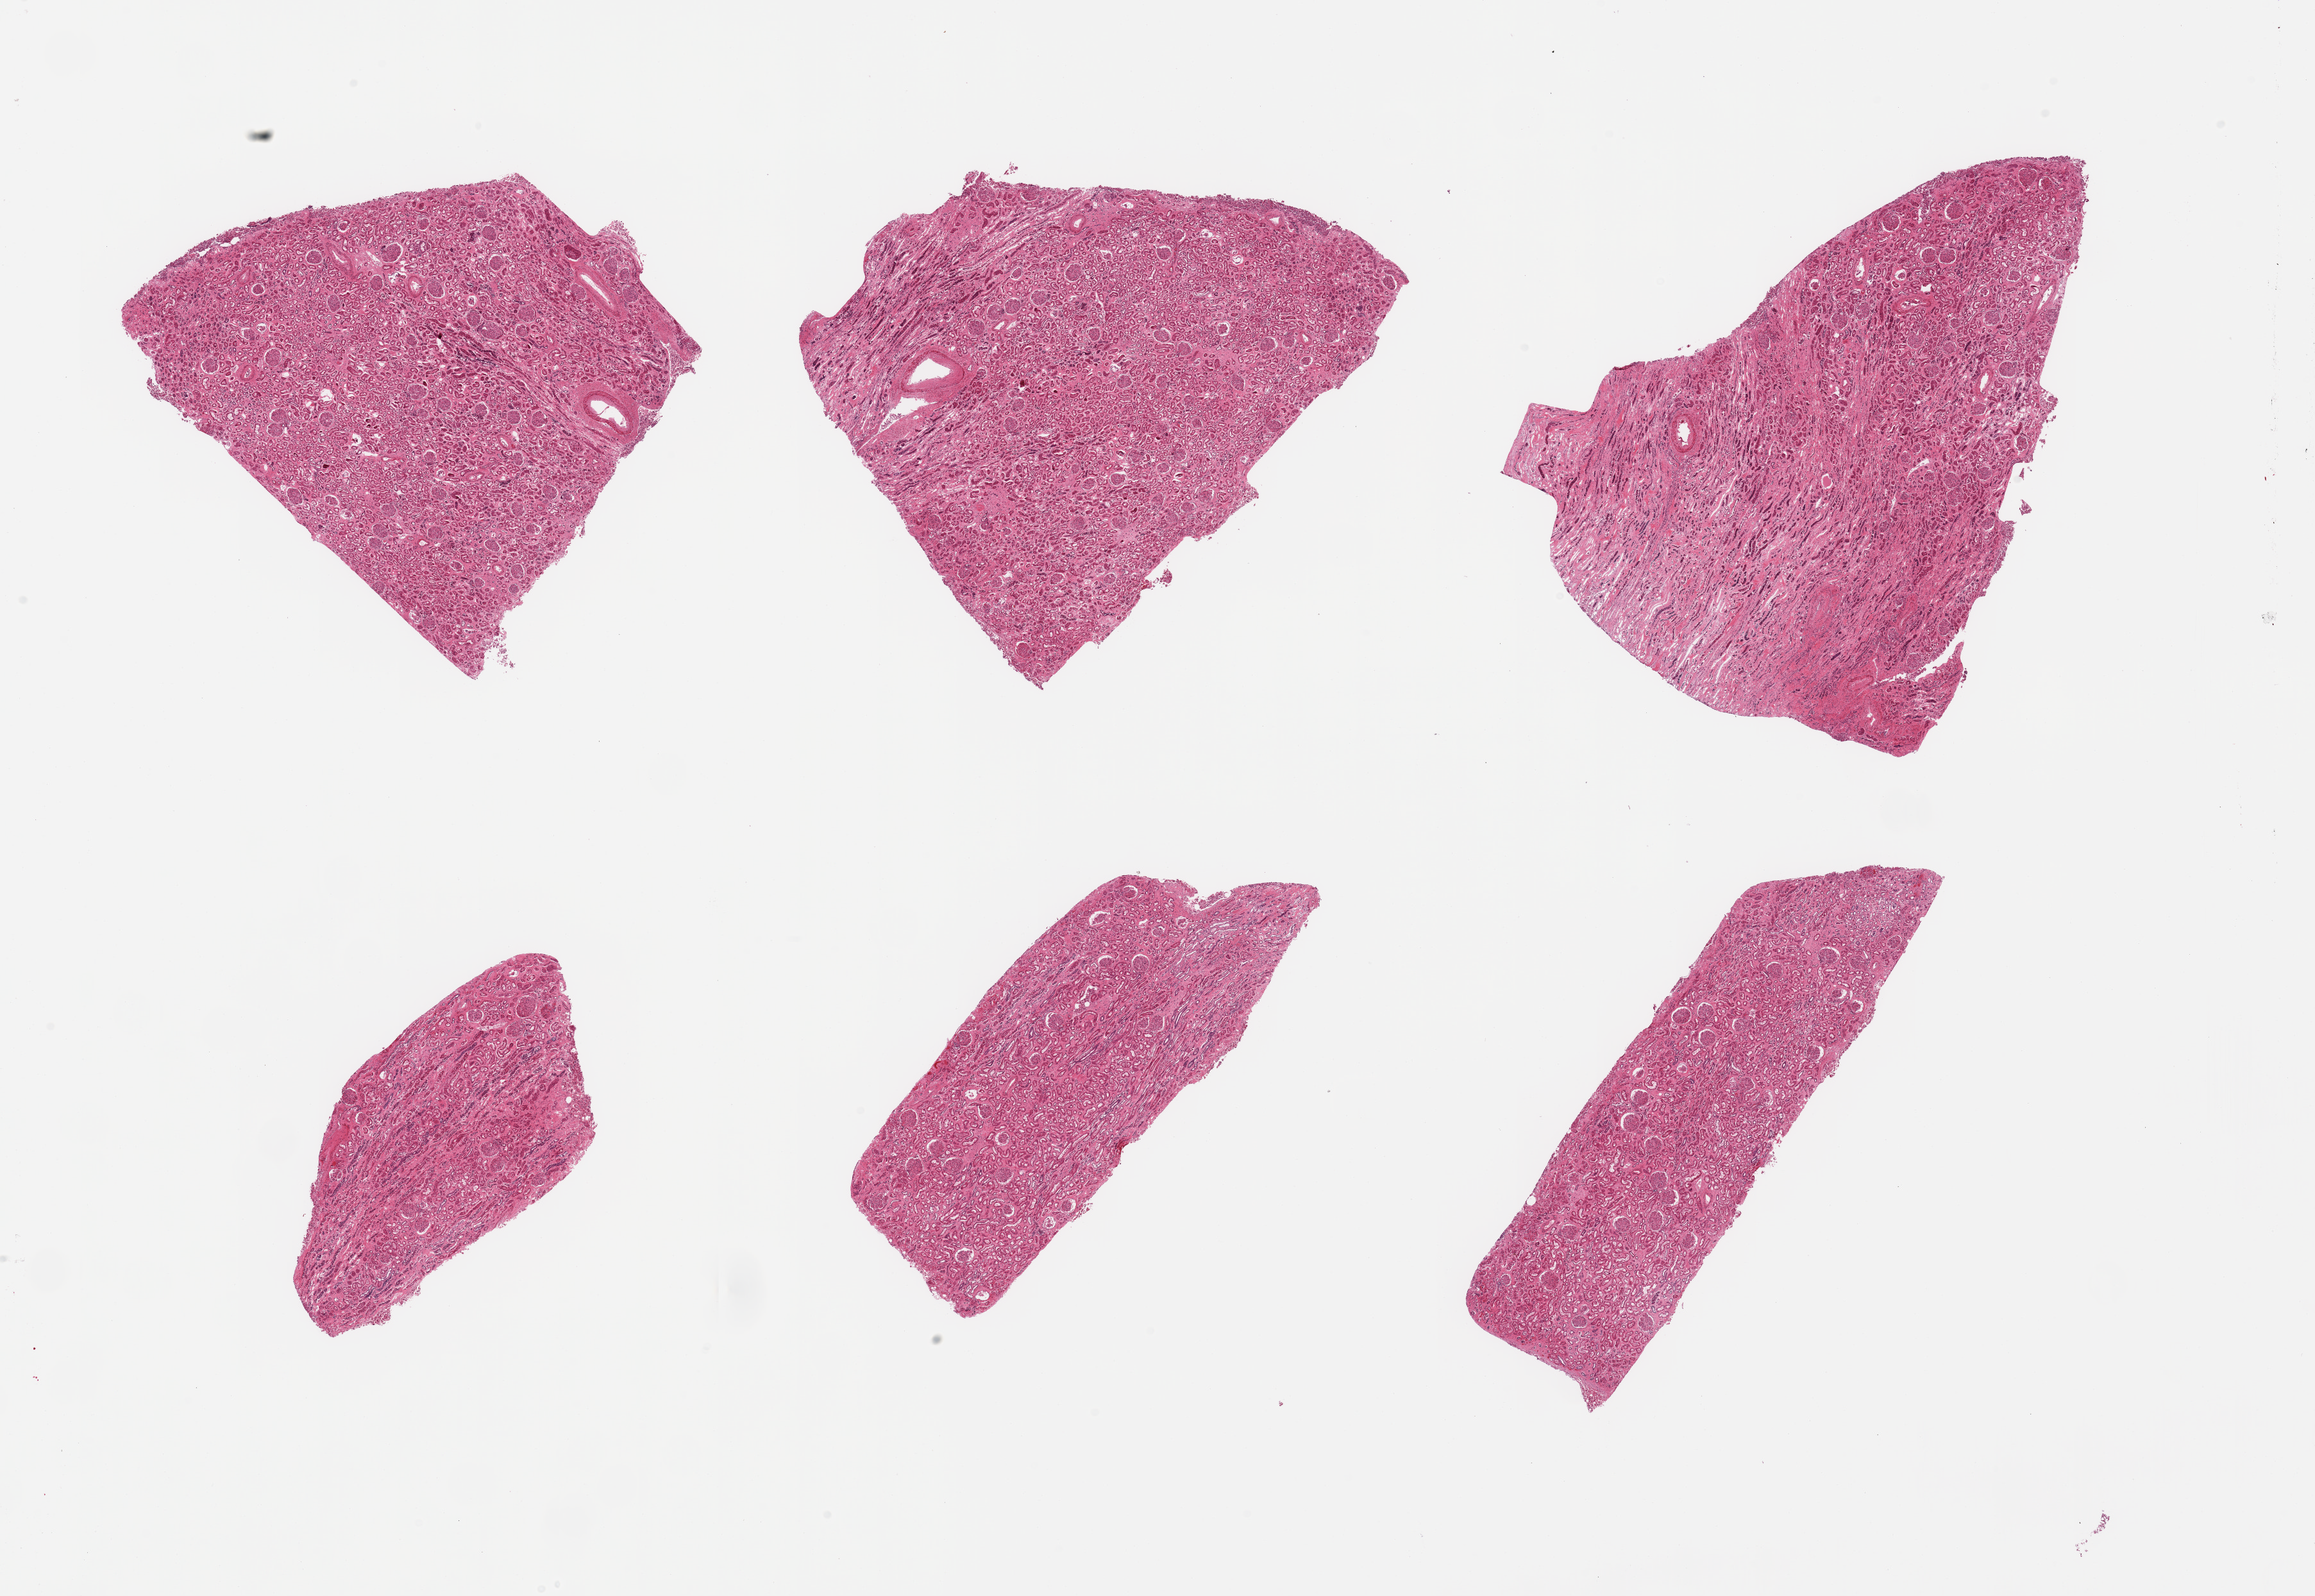
Digitized hematoxylin and eosin (H&E)-stained section, brightfield, low-resolution overview of the scanned area, about 28.5 x 19.7 mm; PAXgene-fixed, paraffin-embedded tissue; section of renal cortex (target tissue); donor tissue sample. Donor sex: male.
- reviewer comment on this tissue sample: 6 pieces; glomeruli in good shape; tubules in variable state of autolysis; no sign of chronic disease